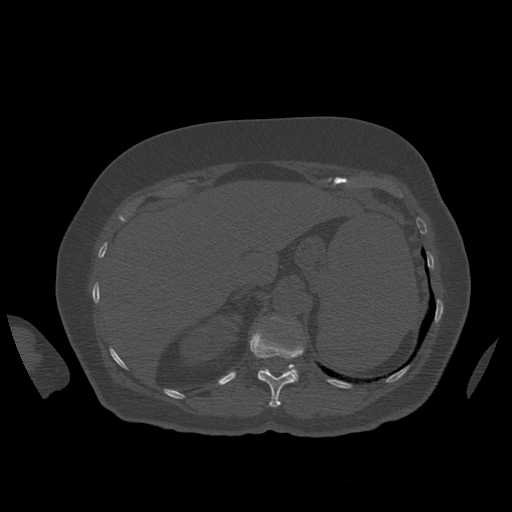
CT including the spine, one axial slice. Slice 296 of 399 in the series (ordered by position). Reconstruction kernel STANDARD. Bone window (W 1800 / L 400 HU). 1.25 mm slice thickness. 512 × 512 image matrix, field of view 404 × 404 mm. Patient age 81 years. Case-level facts recorded for this patient, not image findings: primary cancer: renal; vertebrae with lytic lesions (as recorded): L1.
Annotated regions visible in this slice (semi-automatic segmentation, software-assisted and operator-edited):
- L1 vertebra: bounding box [x1, y1, x2, y2] px = [271, 317, 299, 378]
- T12 vertebra: [250, 331, 304, 408]